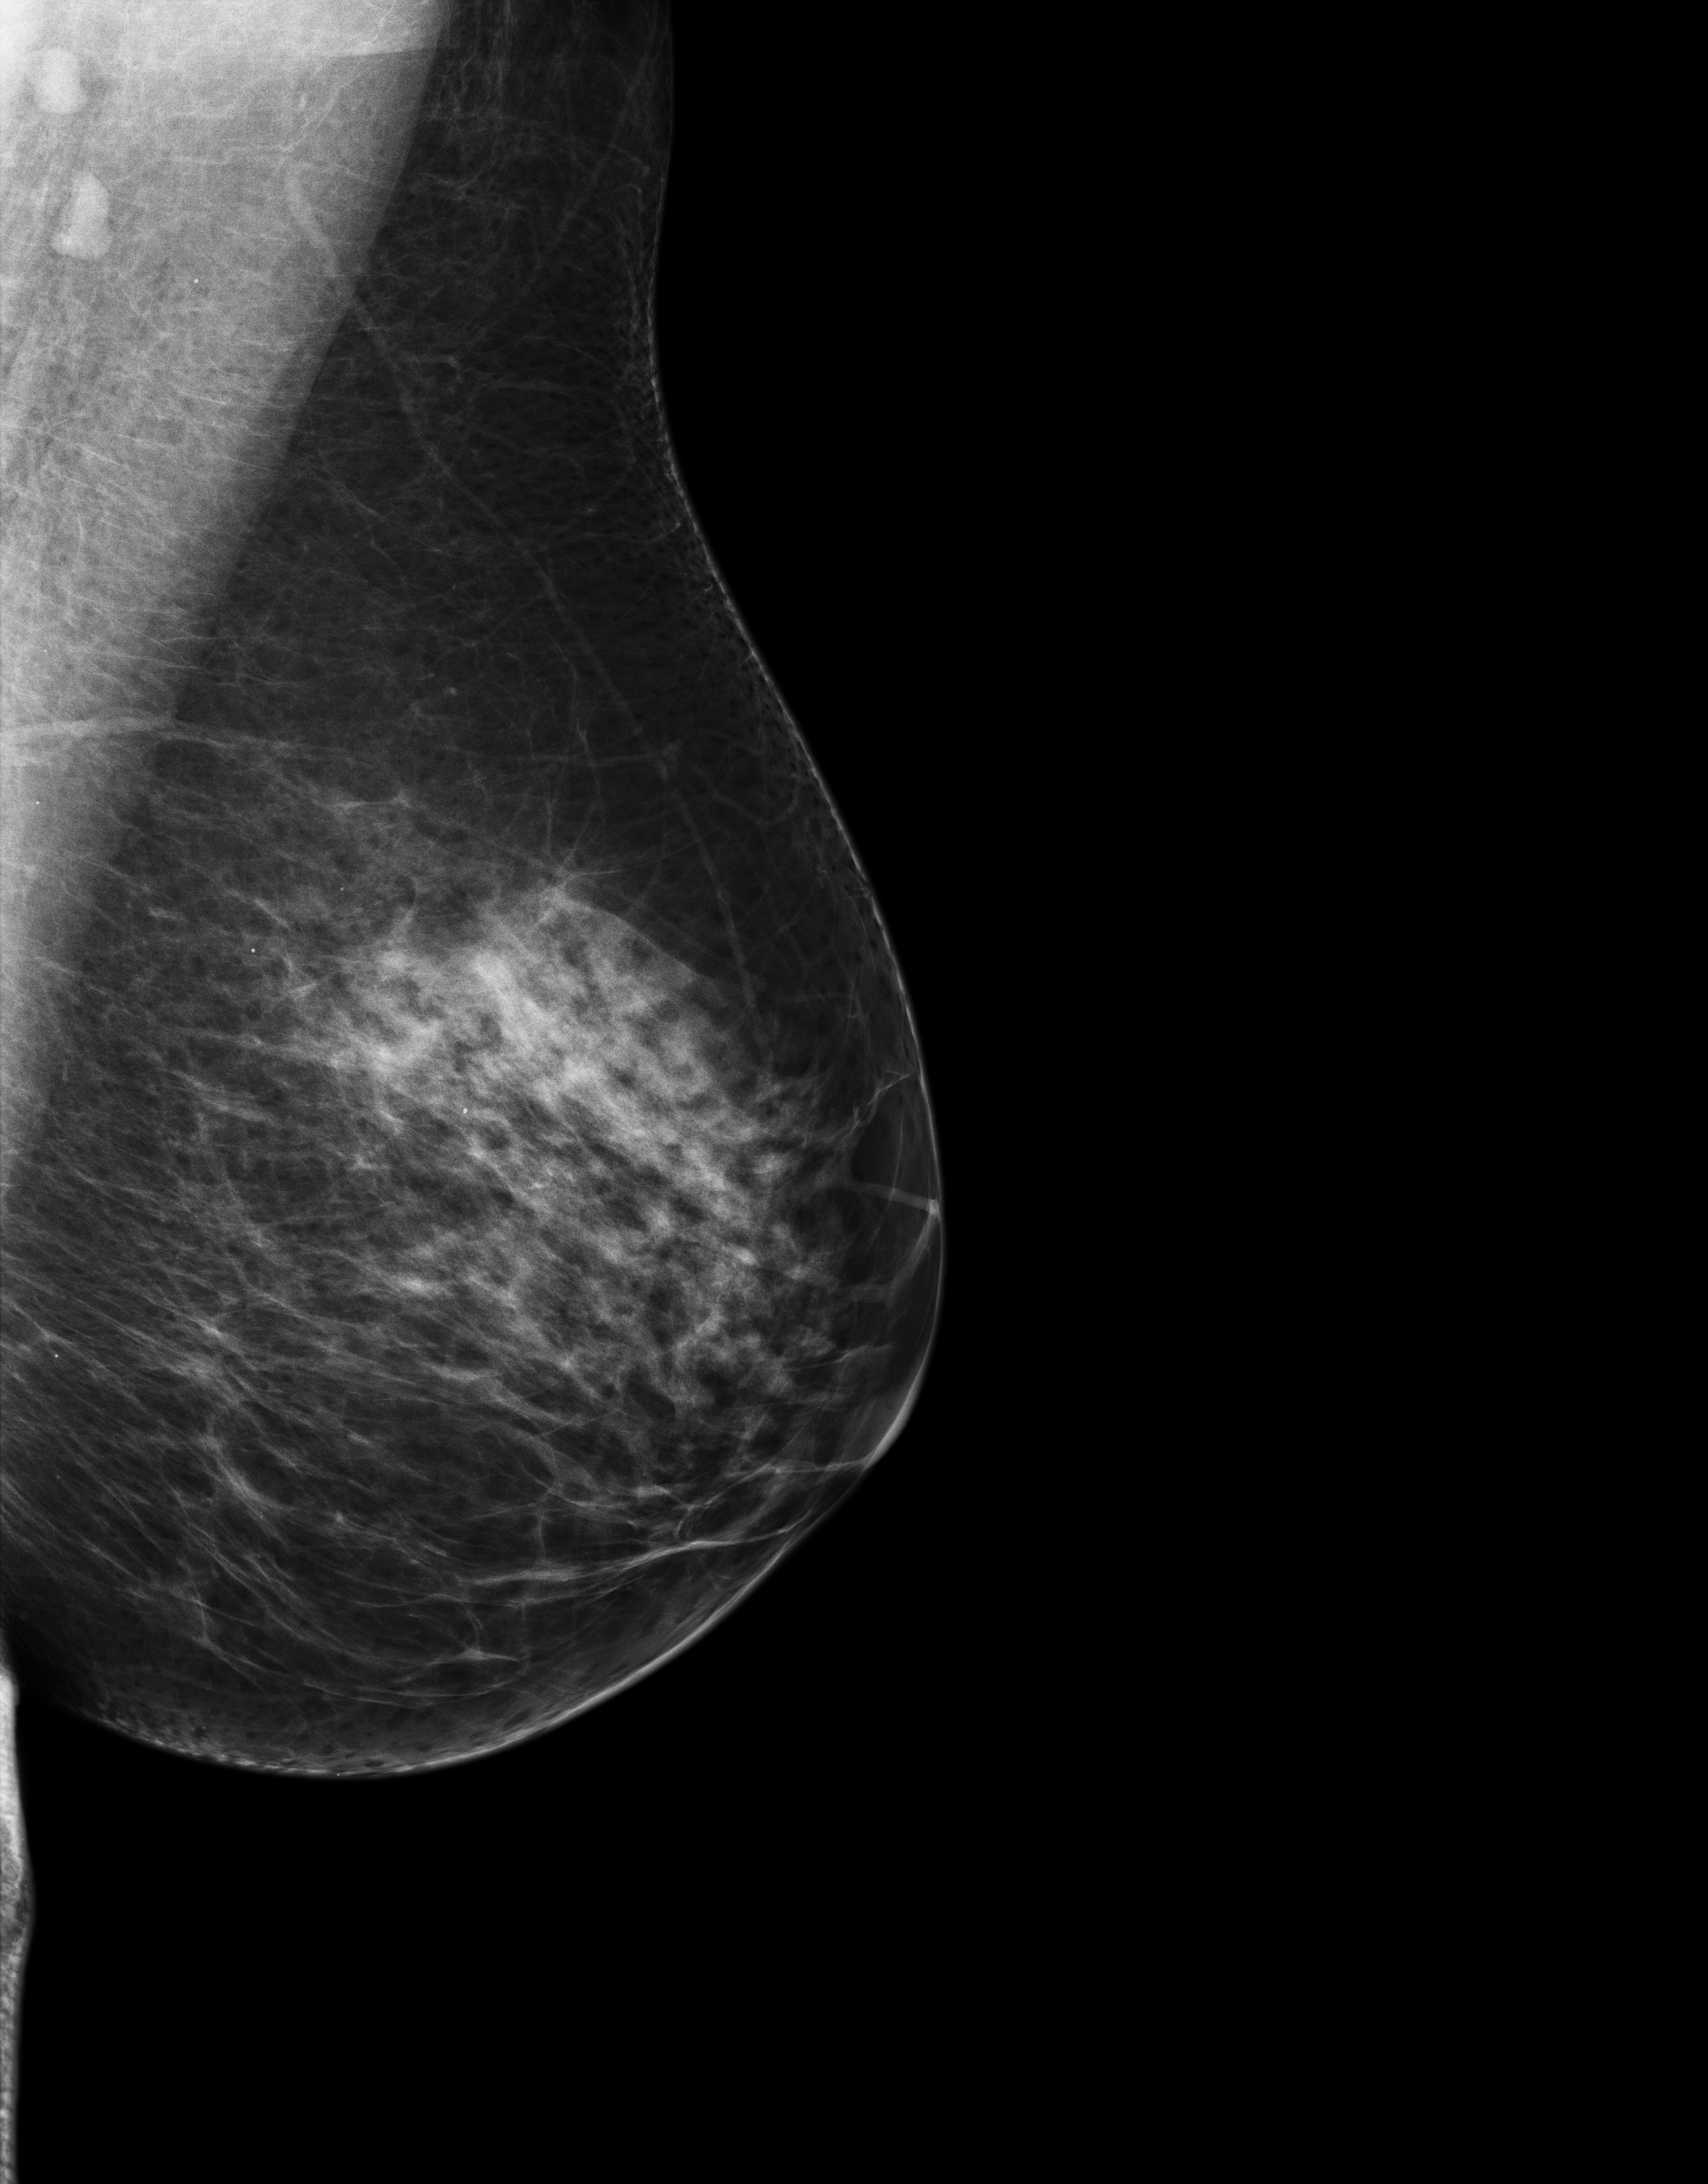
Annual screening mammography examination, compressed breast thickness 69 mm. Patient: female, 57 years.
Image type: full-field digital mammogram. Breast: left. Projection: medio-lateral oblique projection. BI-RADS breast density category at the screening exam (both breasts, scale 1–4): 2. Final BI-RADS assessment for this screening round (tomosynthesis exam, both breasts): category 1. Recall: no recall after this screen.